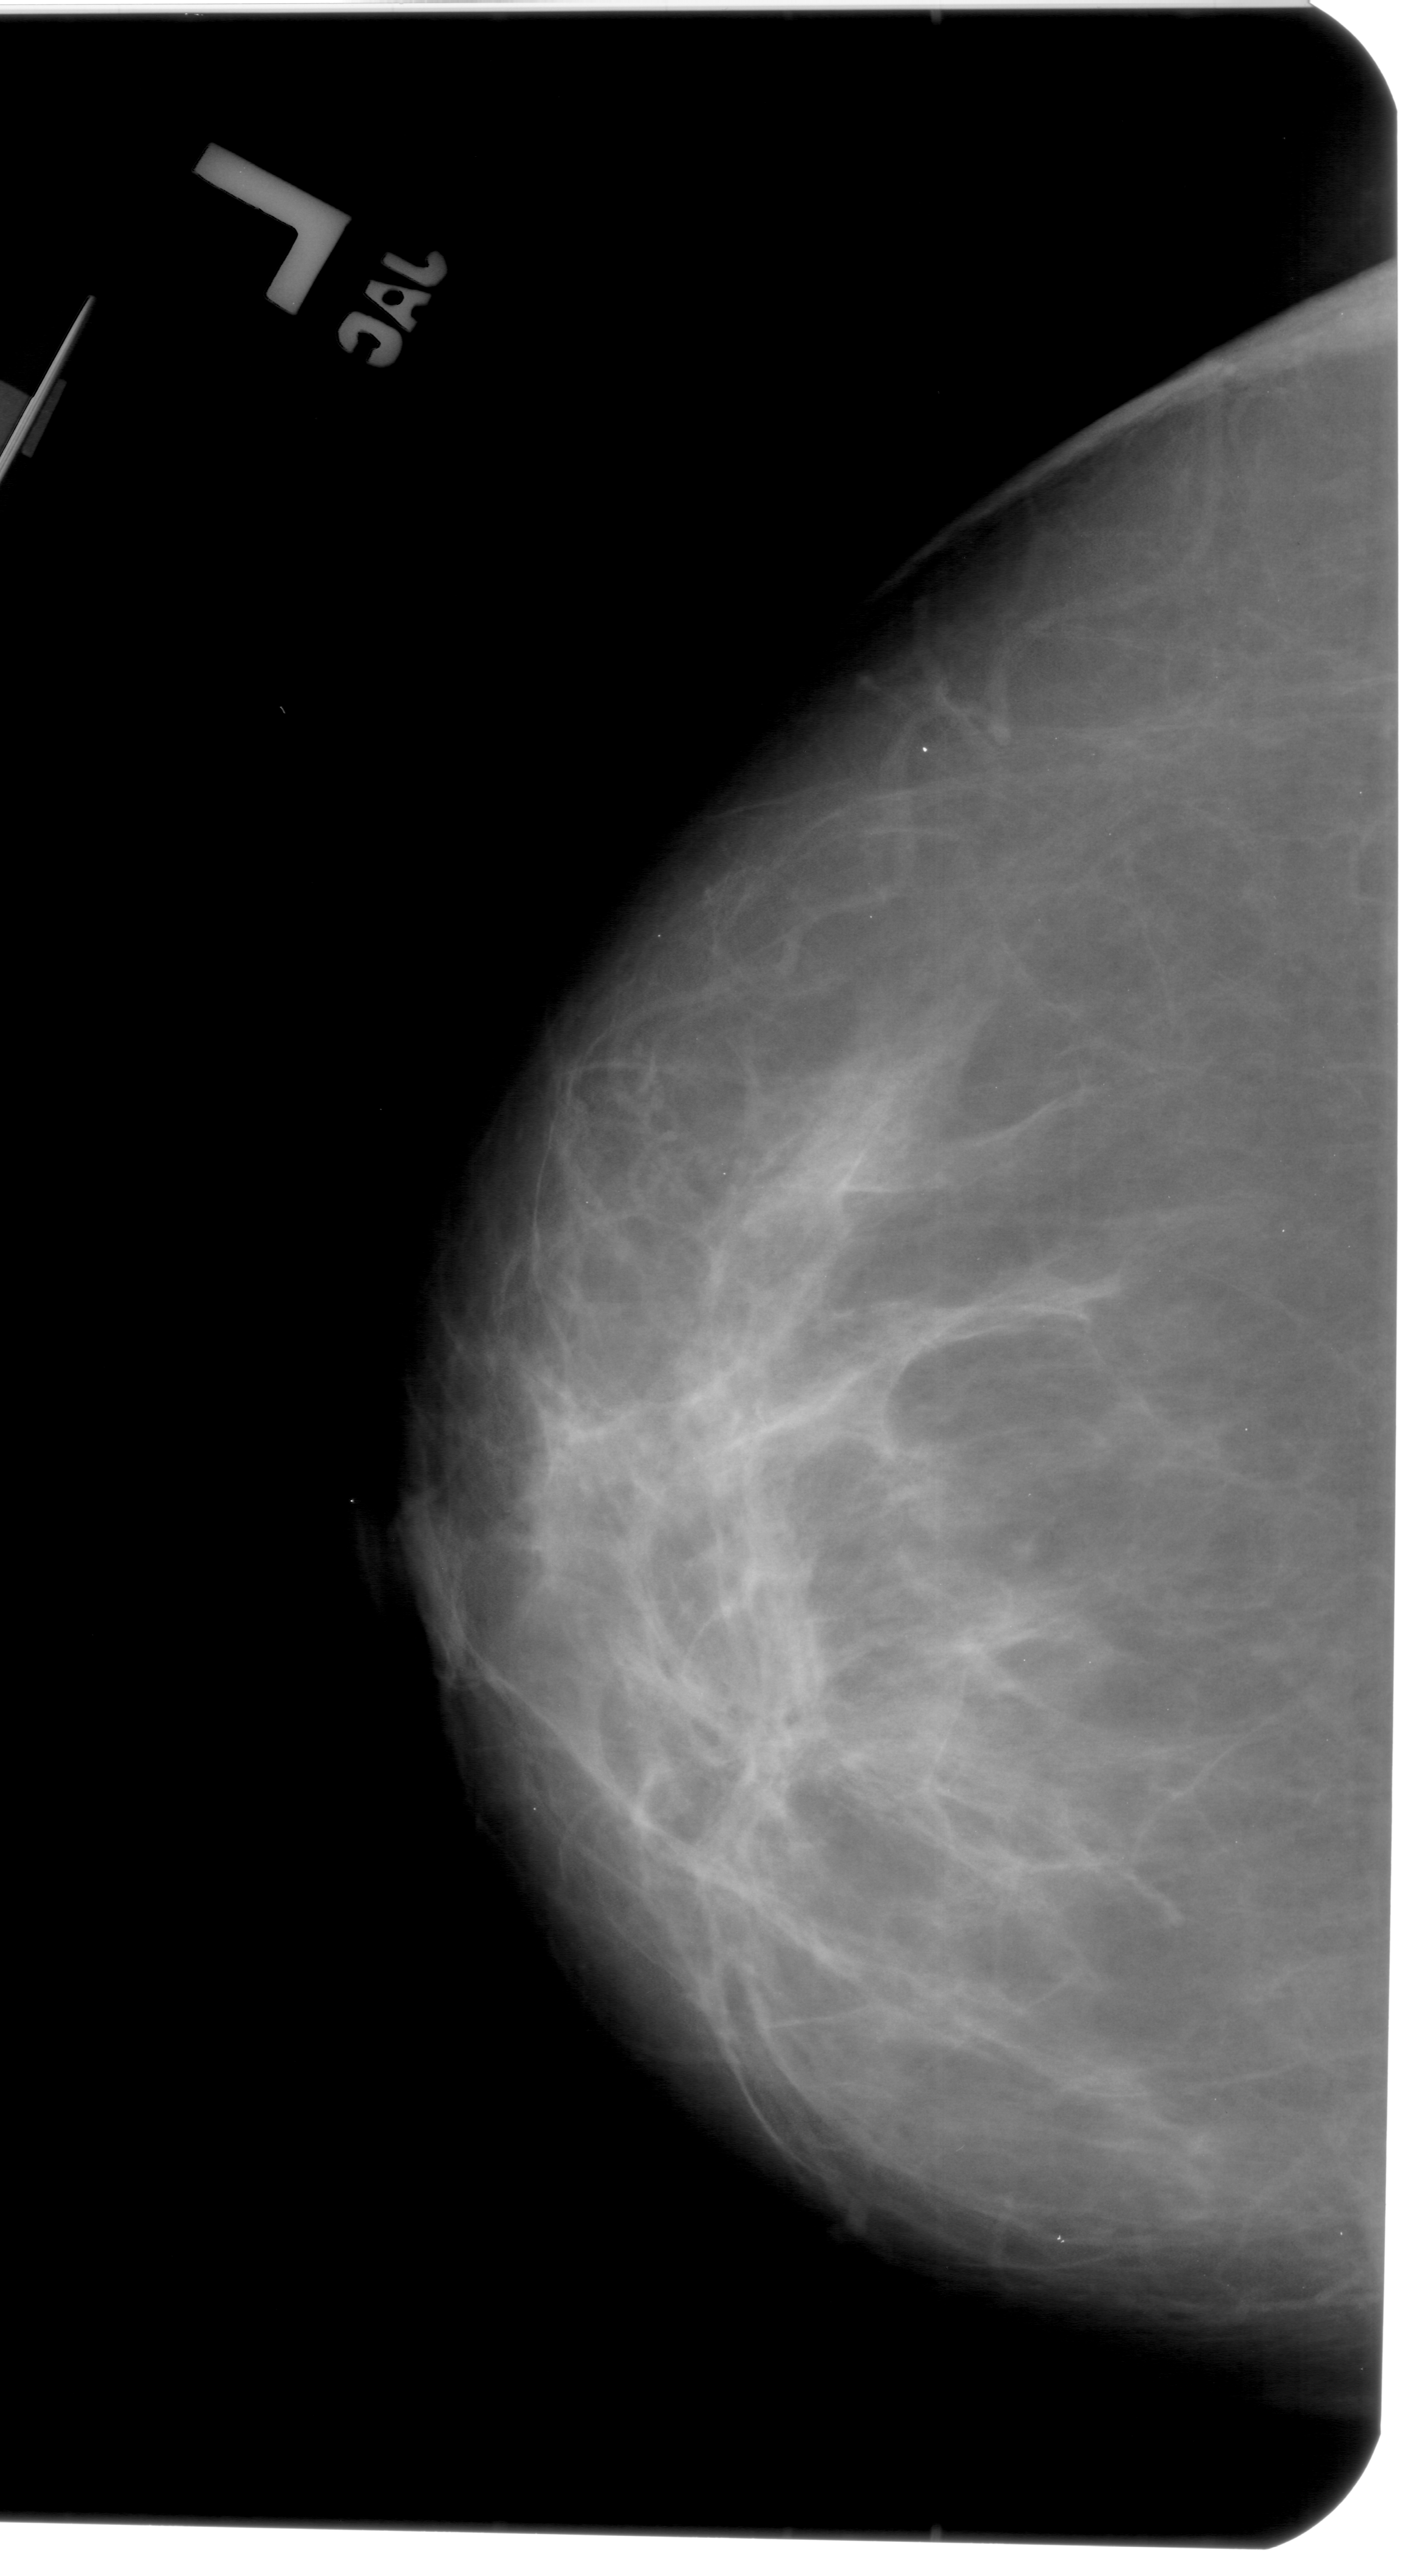
Mammogram (digitized film); left breast; CC view; 1401 × 2576 image matrix.
Expert-marked regions of interest on this image (one box per marked abnormality):
- mass, shape architectural distortion, margins ill defined; BI-RADS assessment category 4; pathology result (as recorded, not read from the image): benign: bounding box (x1, y1, x2, y2) in pixels: (664, 1641, 845, 1842)